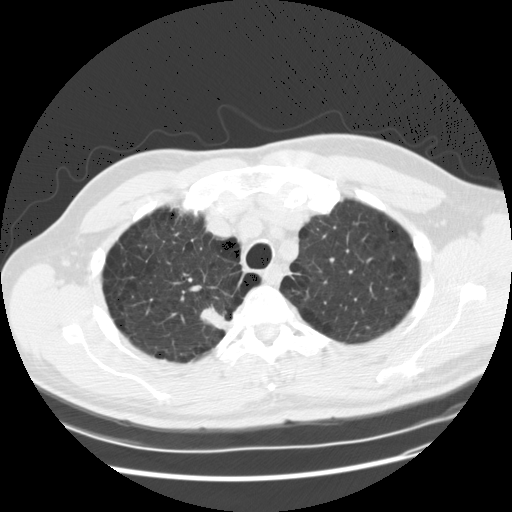
Axial slice from a low-dose chest CT screening exam, baseline annual screen, lung window (W 1500 / L -600 HU), slice 26 of 132 in the series, 512 × 512 image matrix. Male, age 61 years at enrolment. Former smoker at enrolment.
• Lesion marked by an expert reader, bounding box (x1, y1, x2, y2) in pixels: (192, 290, 238, 341).
• Reader record for this screening exam (exam-level; its link to the box is not recorded): non-calcified nodule or mass ≥4 mm, right upper lobe, 19 × 13 mm, poorly defined margins, soft tissue attenuation.
• Official screen result: positive, change unspecified: nodule(s) >= 4 mm or enlarging nodule(s), mass(es), or other non-specific abnormalities suspicious for lung cancer.
• Lung cancer was diagnosed 62 days after this screen: squamous cell carcinoma, NOS, right upper lobe, poorly differentiated (G3), stage IA (AJCC 6th edition), 20 mm at pathology.